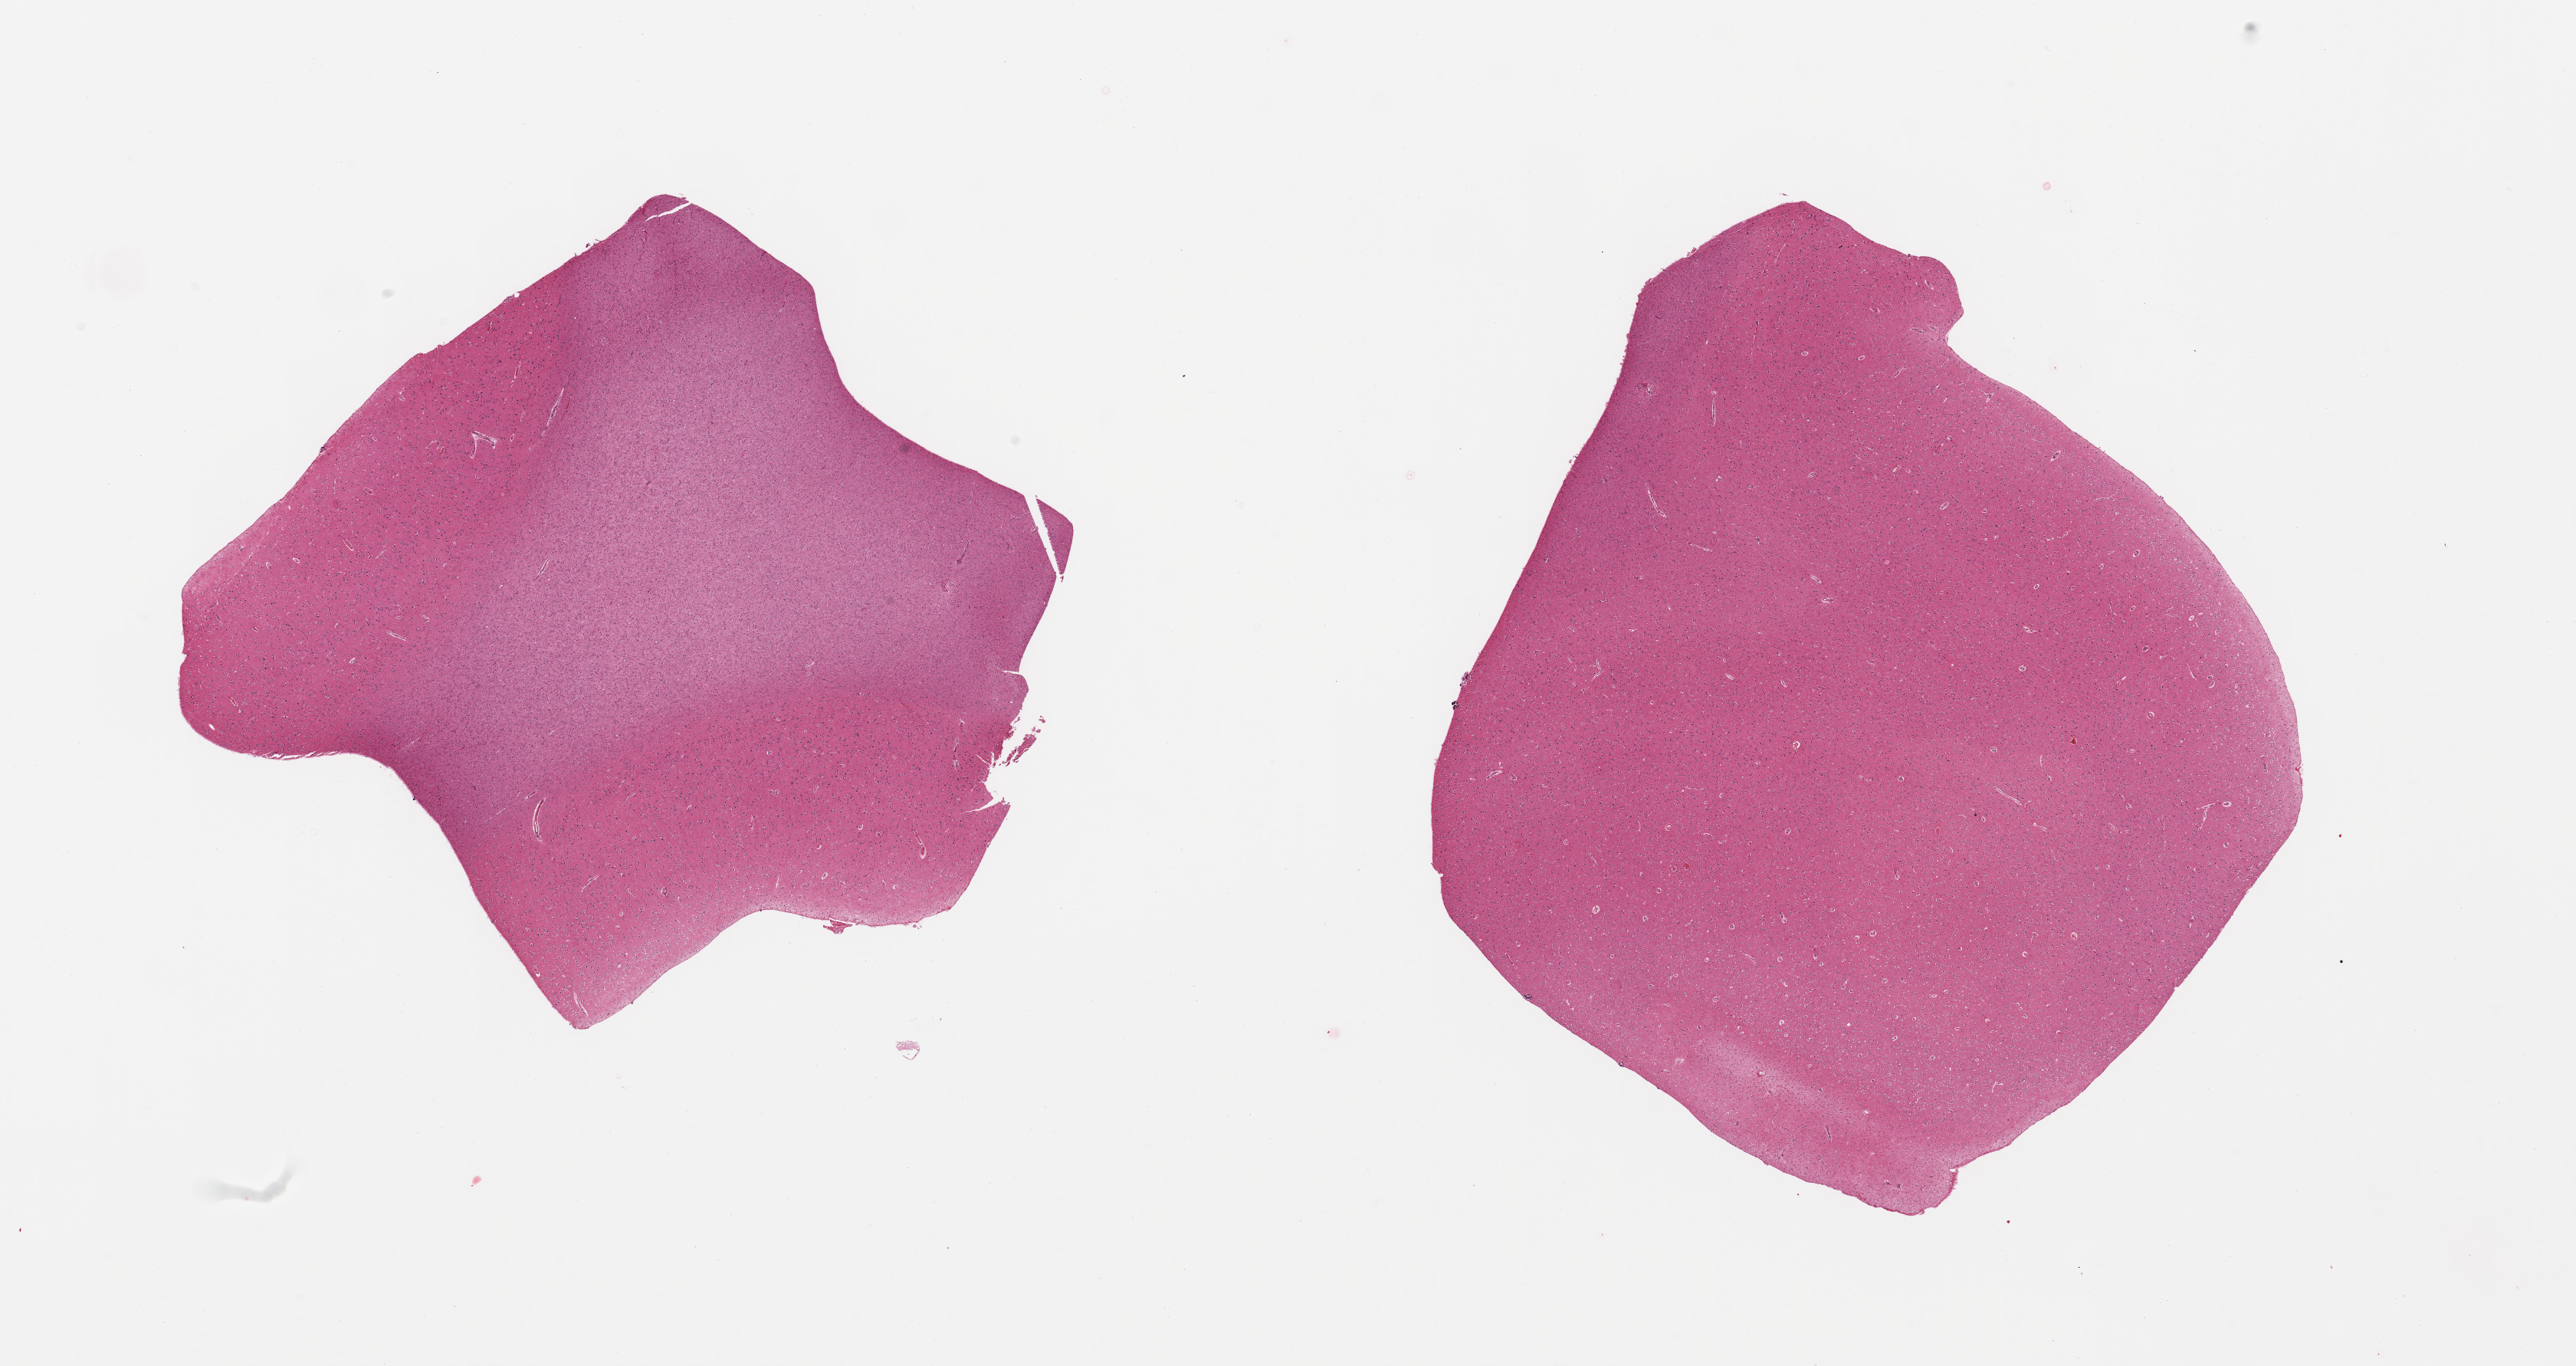
Digitized haematoxylin and eosin-stained section, shown as a low-resolution overview of the whole scanned area (about 26.6 x 14.1 mm, slide scanned at 20x), PAXgene-fixed paraffin-embedded (PFPE) section, section of cerebral cortex (target tissue), tissue donor sample. Male donor.
Pathologist's review note for this sample: 2 fragmented pieces.